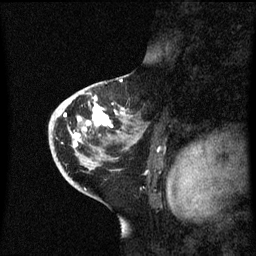
Breast MRI (dynamic contrast-enhanced), one sagittal slice; position 36 of 60 along the scan axis; dynamic contrast-enhanced series, image 2 of 3 at this slice position (ordered by acquisition); 1.5 T; TE 4.2 ms, TR 8.4 ms; 2.3 mm slice thickness; 256 × 256 image matrix, field of view 200 × 200 mm. Patient: female, 46 years. Case-level facts recorded for this patient, not image findings: setting: breast cancer imaged before/during neoadjuvant chemotherapy; receptor status: HER2-positive.
Annotated regions visible in this slice (semi-automatic segmentation, software-assisted and operator-edited):
- analysis volume of interest (the breast-tissue region the enhancement analysis was run in; not a lesion): bounding box [x1, y1, x2, y2] px = [50, 86, 145, 171]
- tumour enhancement mask (voxels above the 70 % enhancement threshold inside the analysis volume of interest): [64, 98, 111, 145]